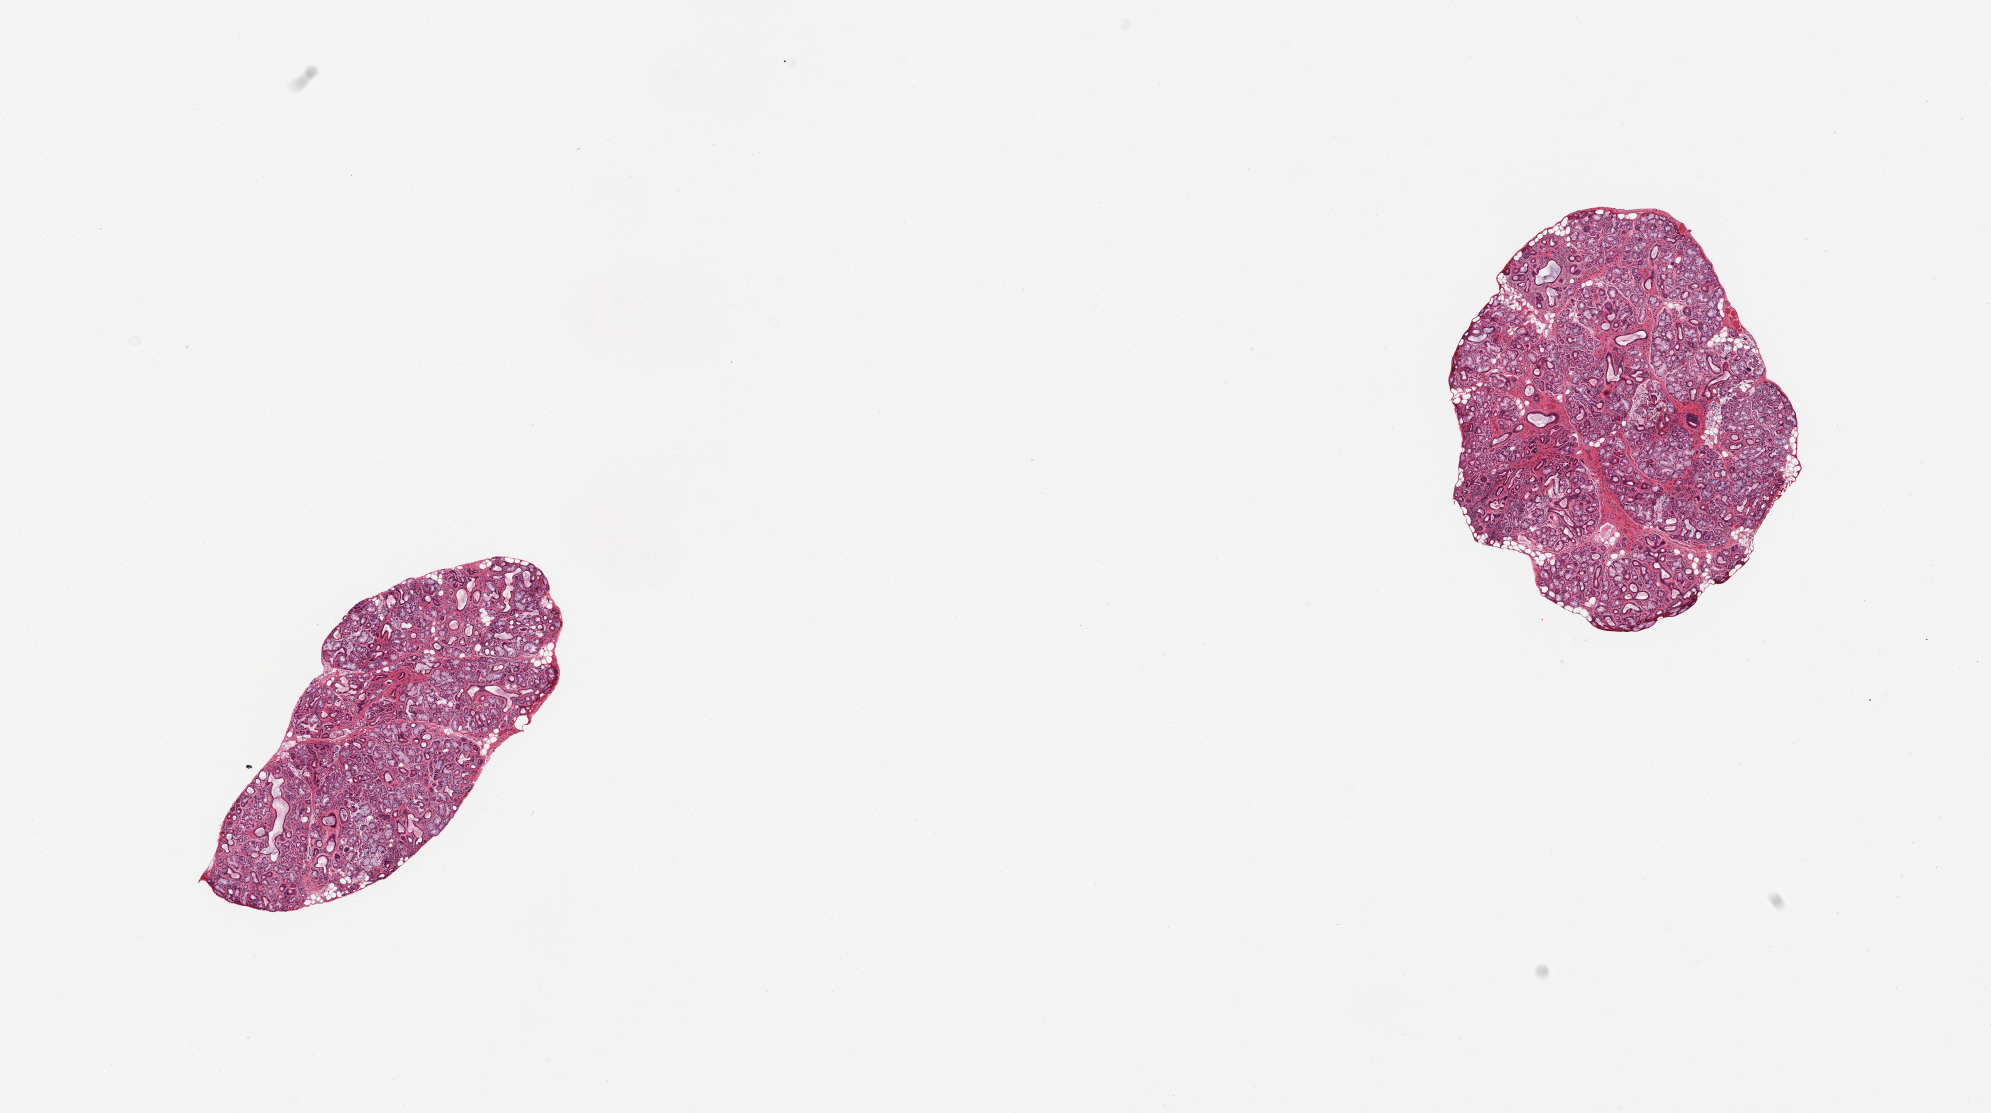
Digitized H&E-stained section, brightfield — shown as a low-resolution overview of the whole scanned area (about 15.8 x 8.8 mm), PAXgene-fixed paraffin-embedded (PFPE) section, sampled site (target tissue): minor salivary gland, tissue donor sample. Donor: female.
Pathologist's review note for this sample: 2 pieces; well dissected glands.